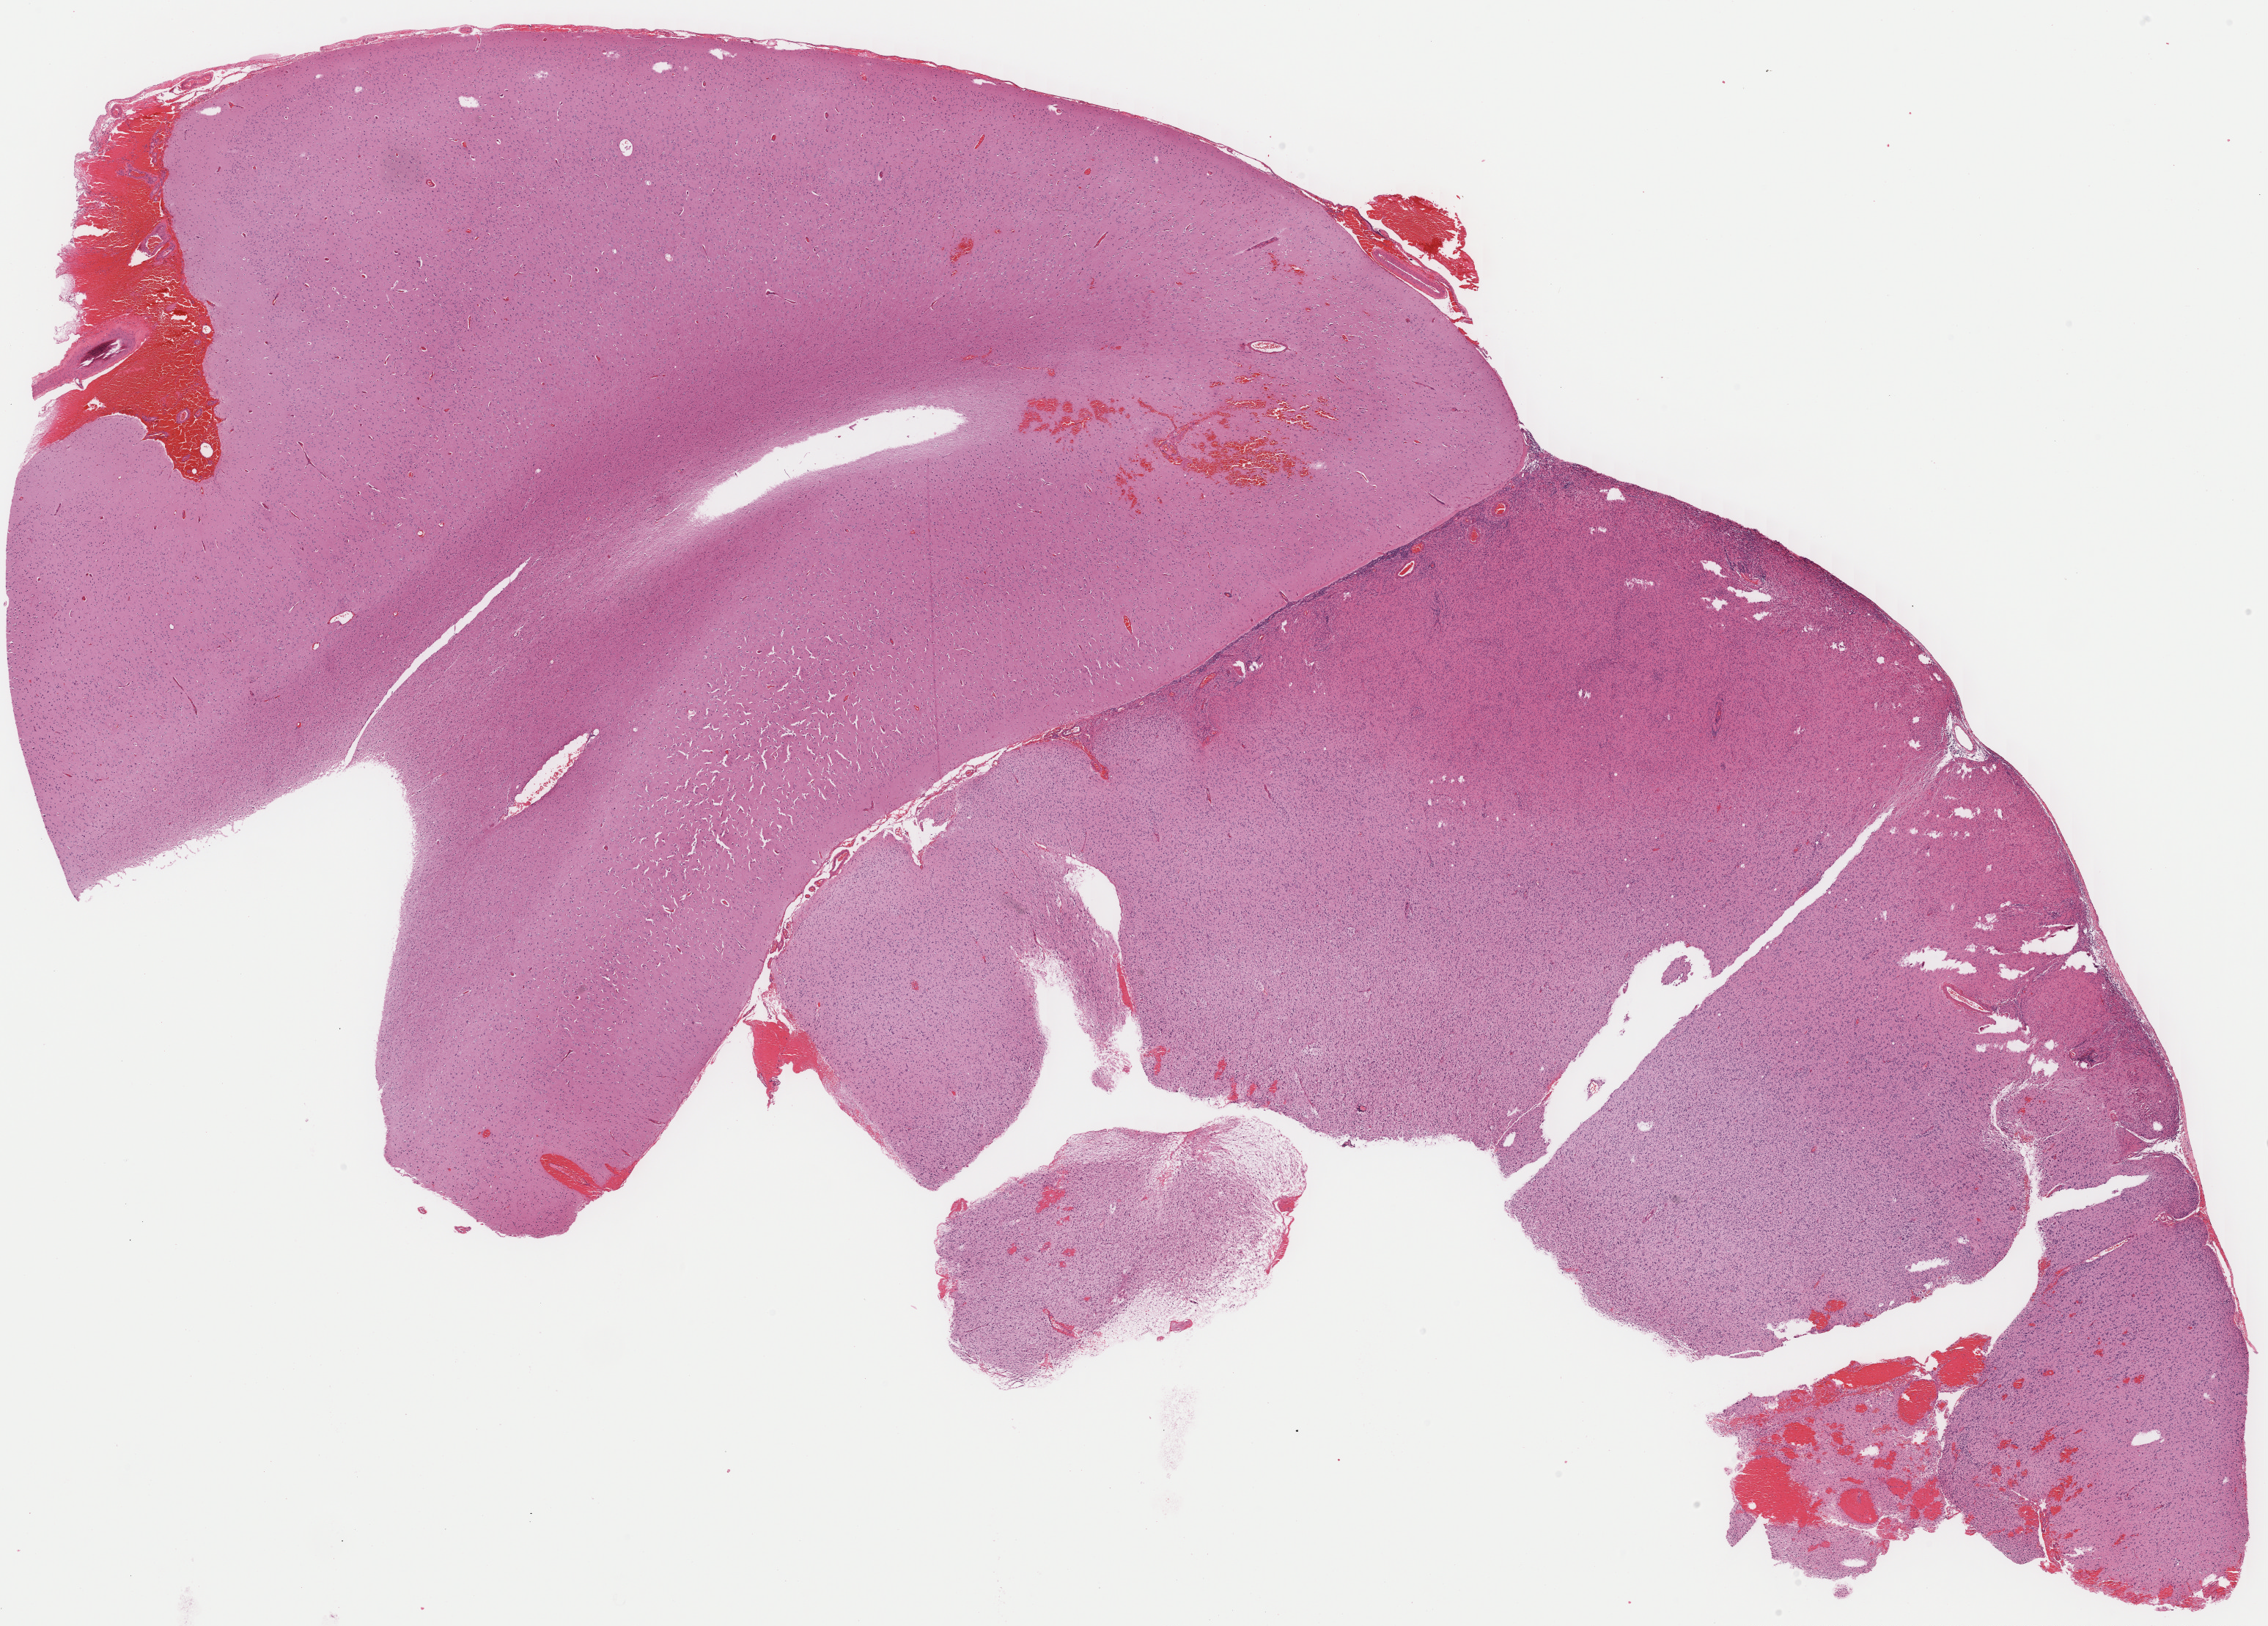
Whole-slide histology image, H&E — whole scanned area (about 24.4 x 17.5 mm) shown as a low-resolution overview, FFPE section, sample: primary tumour, brain. Male patient; age at initial diagnosis 38 years.
Histologic diagnosis: Astrocytoma, anaplastic.